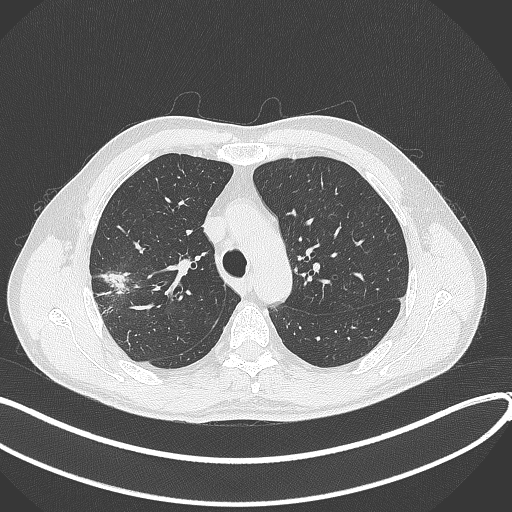
Chest CT, one axial slice; slice 304 of 381 in the series (ordered by position); 120 kVp; lung window (W 1500 / L -600 HU); 1 mm slice thickness; 512 × 512 image matrix, field of view 400 × 400 mm. Patient: male, 62 years. Case-level facts recorded for this patient, not image findings: clinical TNM (as recorded): T1c N0 M0; histopathological grade: G2-3.
Structures marked on this image (bounding box drawn by a radiologist):
- lung tumour (recorded histology: adenocarcinoma): bounding box <101,265,131,295> (left, top, right, bottom; pixels)